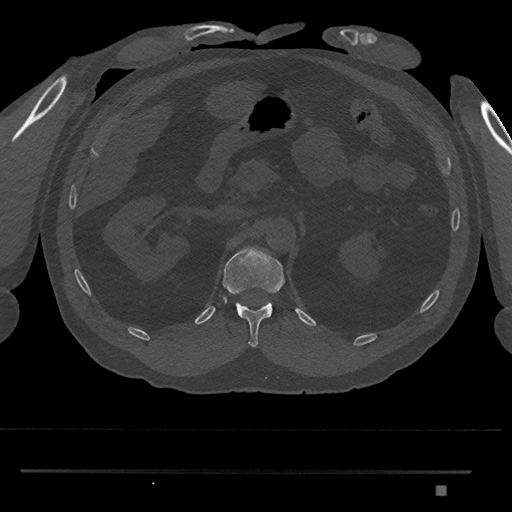
CT including the spine, one axial slice; slice 874 of 1134 in the series (ordered by position); reconstruction kernel Br40s/3; 120 kVp; bone window (W 1800 / L 400 HU); 0.5 mm slice thickness; 512 × 512 image matrix, field of view 429 × 429 mm. Male patient, age 65 years. Case-level facts recorded for this patient, not image findings: primary cancer: prostate.
Annotated regions visible in this slice (semi-automatically segmented with operator editing):
- T12 vertebra: bounding box (x1, y1, x2, y2) in pixels: (222, 247, 285, 347)